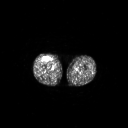
FDG PET of an extremity soft-tissue mass (from a PET/CT study), one axial slice. 3.27 mm slice thickness. 128 × 128 image matrix, field of view 700 × 700 mm. Male patient, age 56 years. From the clinical record (not read from this slice): histological type: pleiomorphic leiomyosarcoma; grade: intermediate; site of the primary tumour: right thigh.
Structures marked on this image (expert contour drawn on MRI and transferred to this co-registered scan by the dataset authors):
- gross tumour volume including surrounding oedema: box from (x=43, y=56) to (x=51, y=62) px